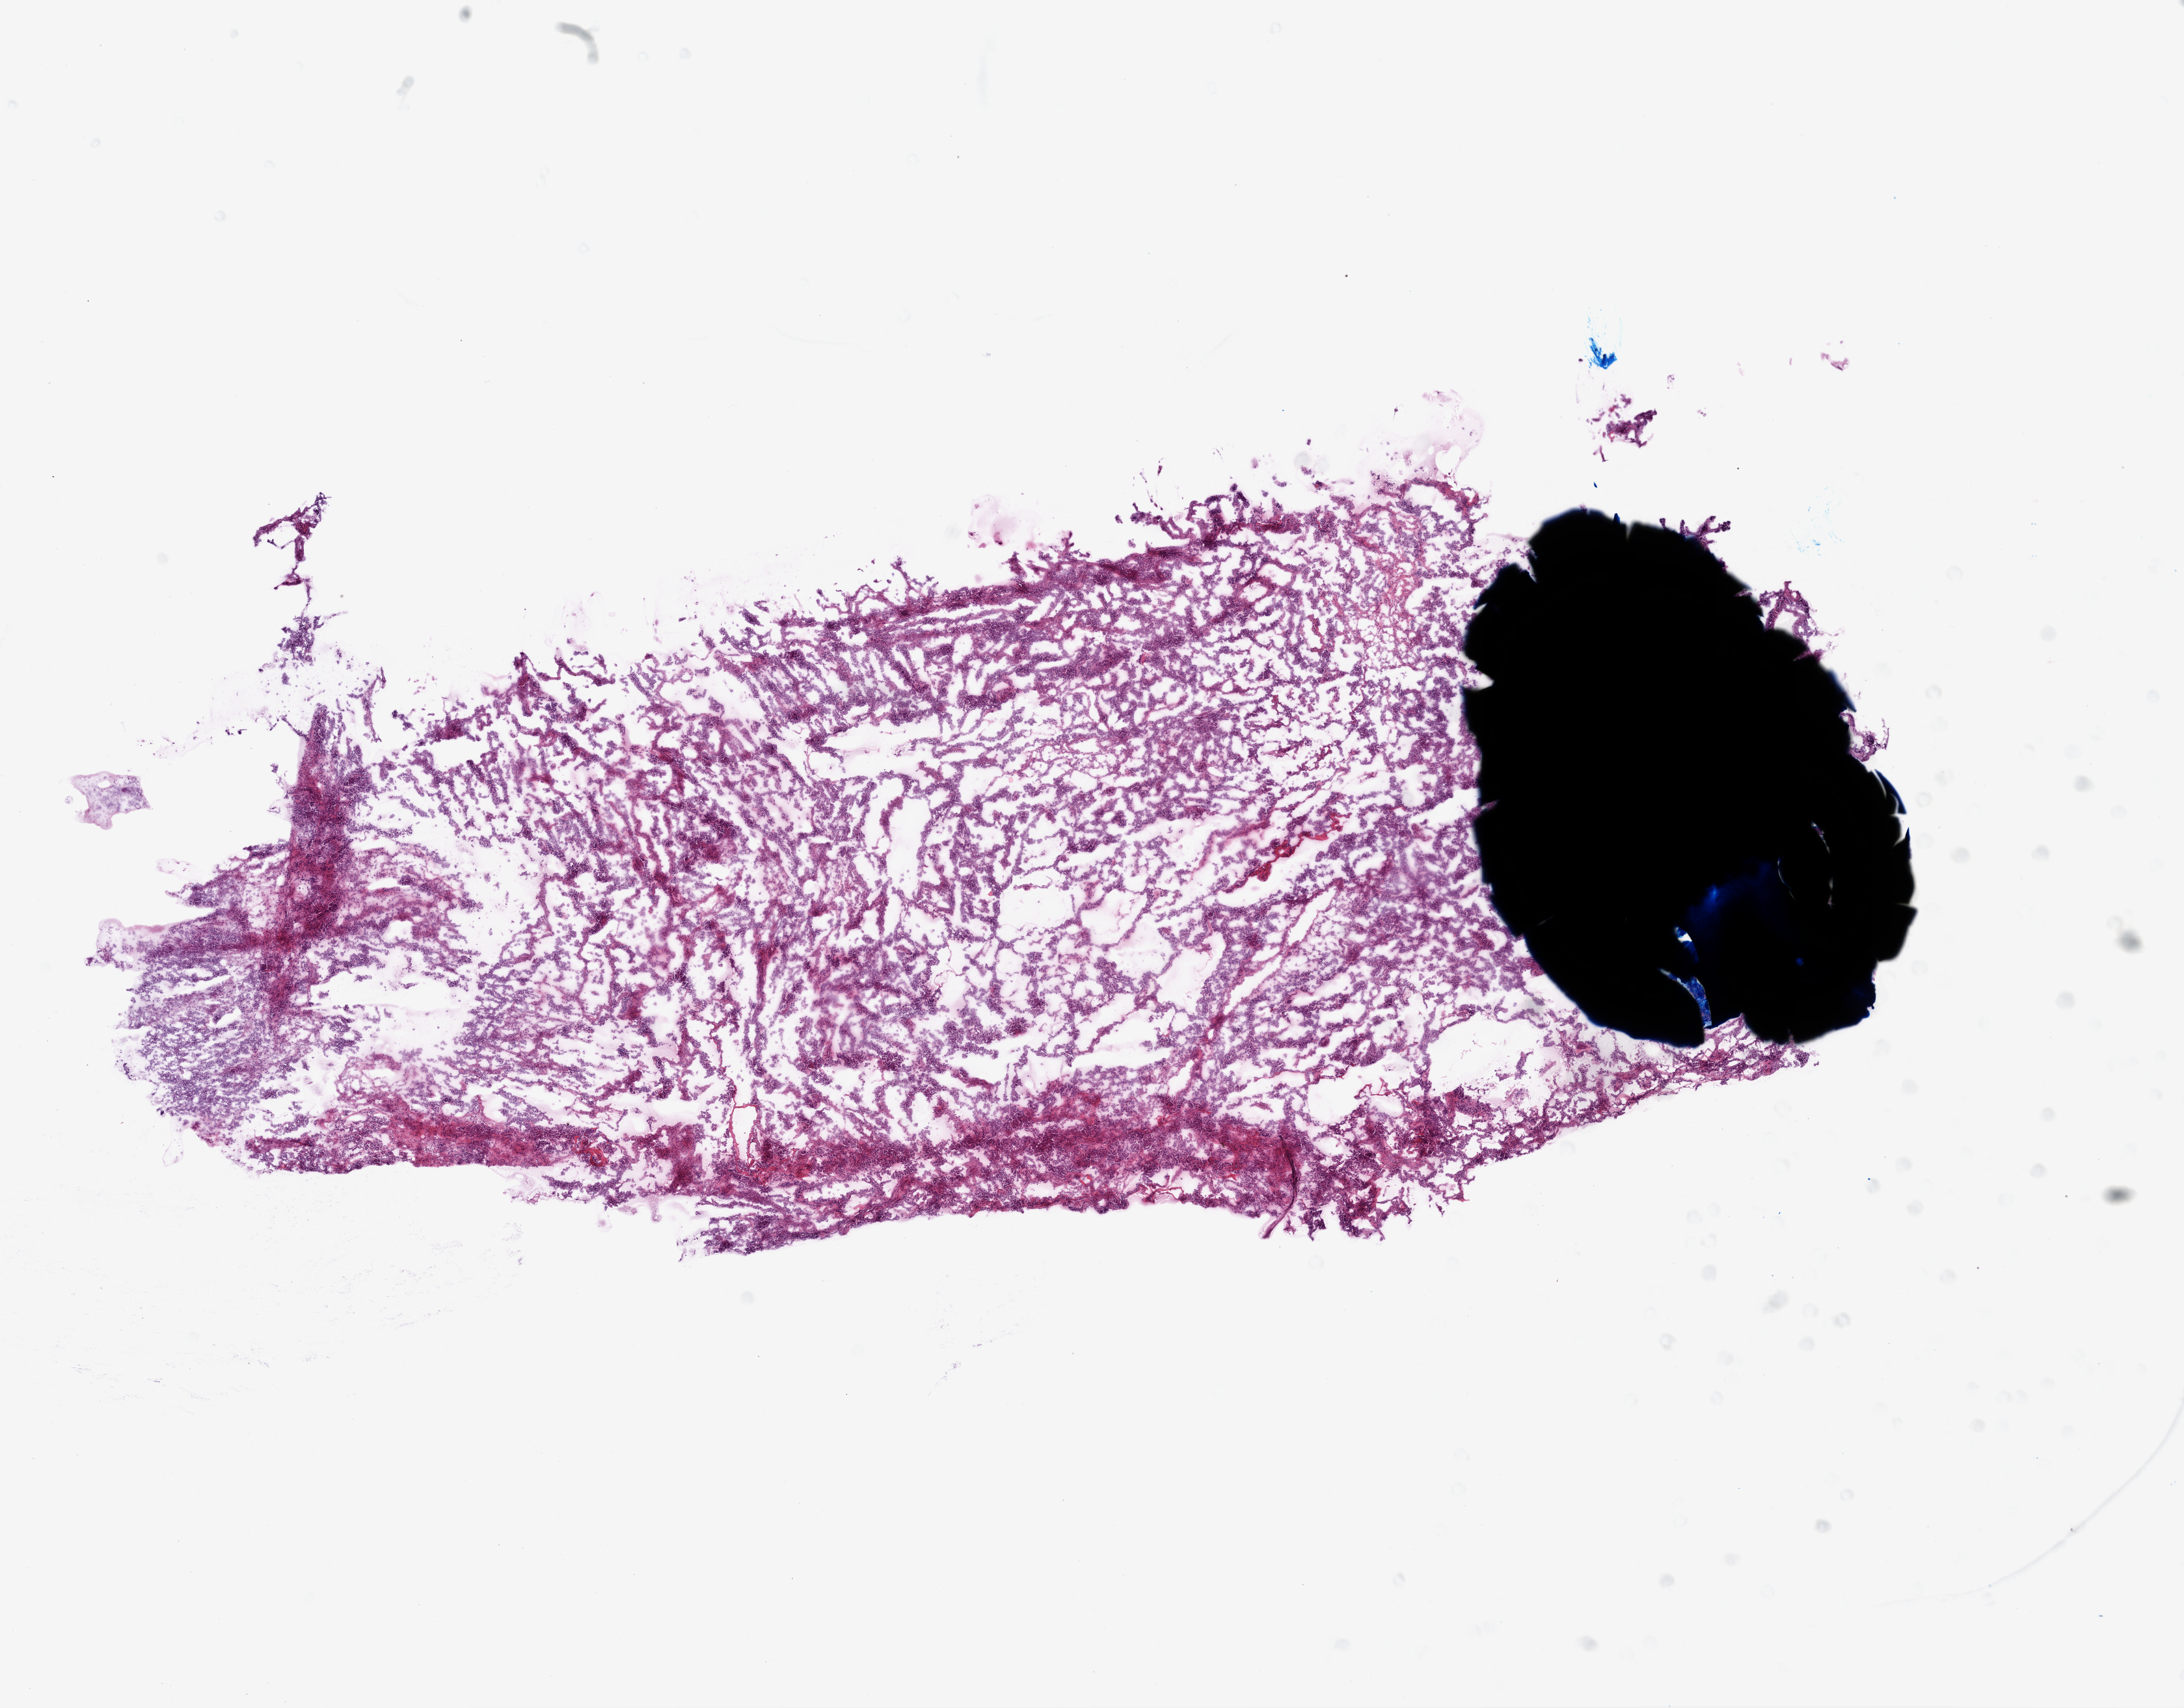
Digitized H&E-stained tissue section (whole slide), shown as a low-resolution overview of the whole scanned area (about 13.5 x 10.6 mm, slide scanned at 20x); frozen section from the top of the tissue portion; ovary, primary tumour sample. Patient: female, age at initial diagnosis 77 years. Histologic grade: G3 (poorly differentiated). Slide review estimates, as recorded: tumour cells 90%, tumour nuclei 90%, normal cells 5%, stromal cells 5%, necrosis 0%. Infiltration values recorded for this section: lymphocyte infiltration 0%, neutrophil infiltration 0%.
Pathologic diagnosis: Serous cystadenocarcinoma, NOS. FIGO stage: IIIC. Laterality: bilateral.